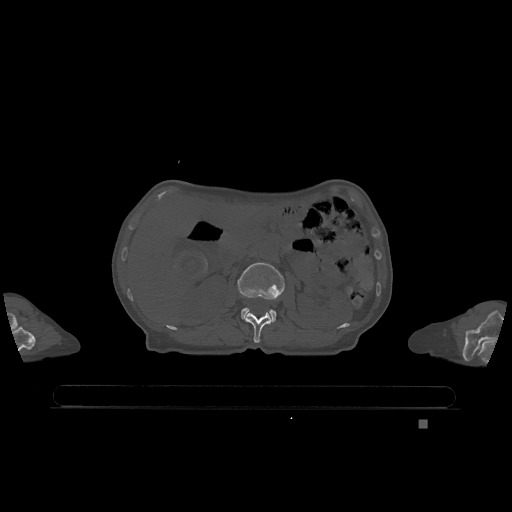
CT including the spine, one axial slice; position 447 of 1317 along the scan axis; bone window (W 1800 / L 400 HU); 0.5 mm slice thickness; 512 × 512 image matrix, field of view 500 × 500 mm. Patient: female, 74 years. Case-level facts recorded for this patient, not image findings: primary cancer: lung; vertebrae with lytic lesions (as recorded): T1, T4, T5, T6, L4, L5.
Outlined on this slice (semi-automatically segmented with operator editing):
- L1 vertebra: box from (x=244, y=313) to (x=272, y=343) px
- L2 vertebra: (x=238, y=262)–(x=285, y=323)